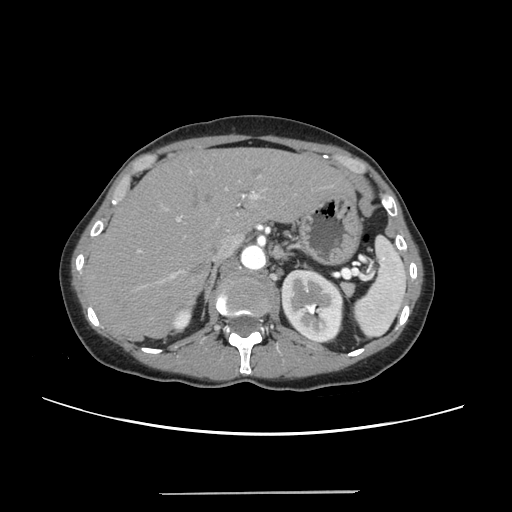
Contrast-enhanced abdominal CT, one axial slice; slice 167 of 240 in the series (ordered by position); 120 kVp; intravenous contrast given; soft-tissue window (W 400 / L 40 HU); 1.25 mm slice thickness; 512 × 512 image matrix, field of view 371 × 371 mm. Female patient, age 60 years. From the clinical record (not read from this slice): diagnosis: colorectal cancer liver metastases, imaged before liver resection; multiple liver metastases: no; largest metastasis: 1.5 cm; disease in both lobes: no.
Outlined on this slice (manually delineated by an expert):
- liver: bounding box (x1, y1, x2, y2) in pixels: (86, 149, 349, 337)
- planned liver remnant (the part of the liver to remain after resection): (86, 149, 348, 336)
- portal vein (with intrahepatic branches): (138, 172, 260, 288)